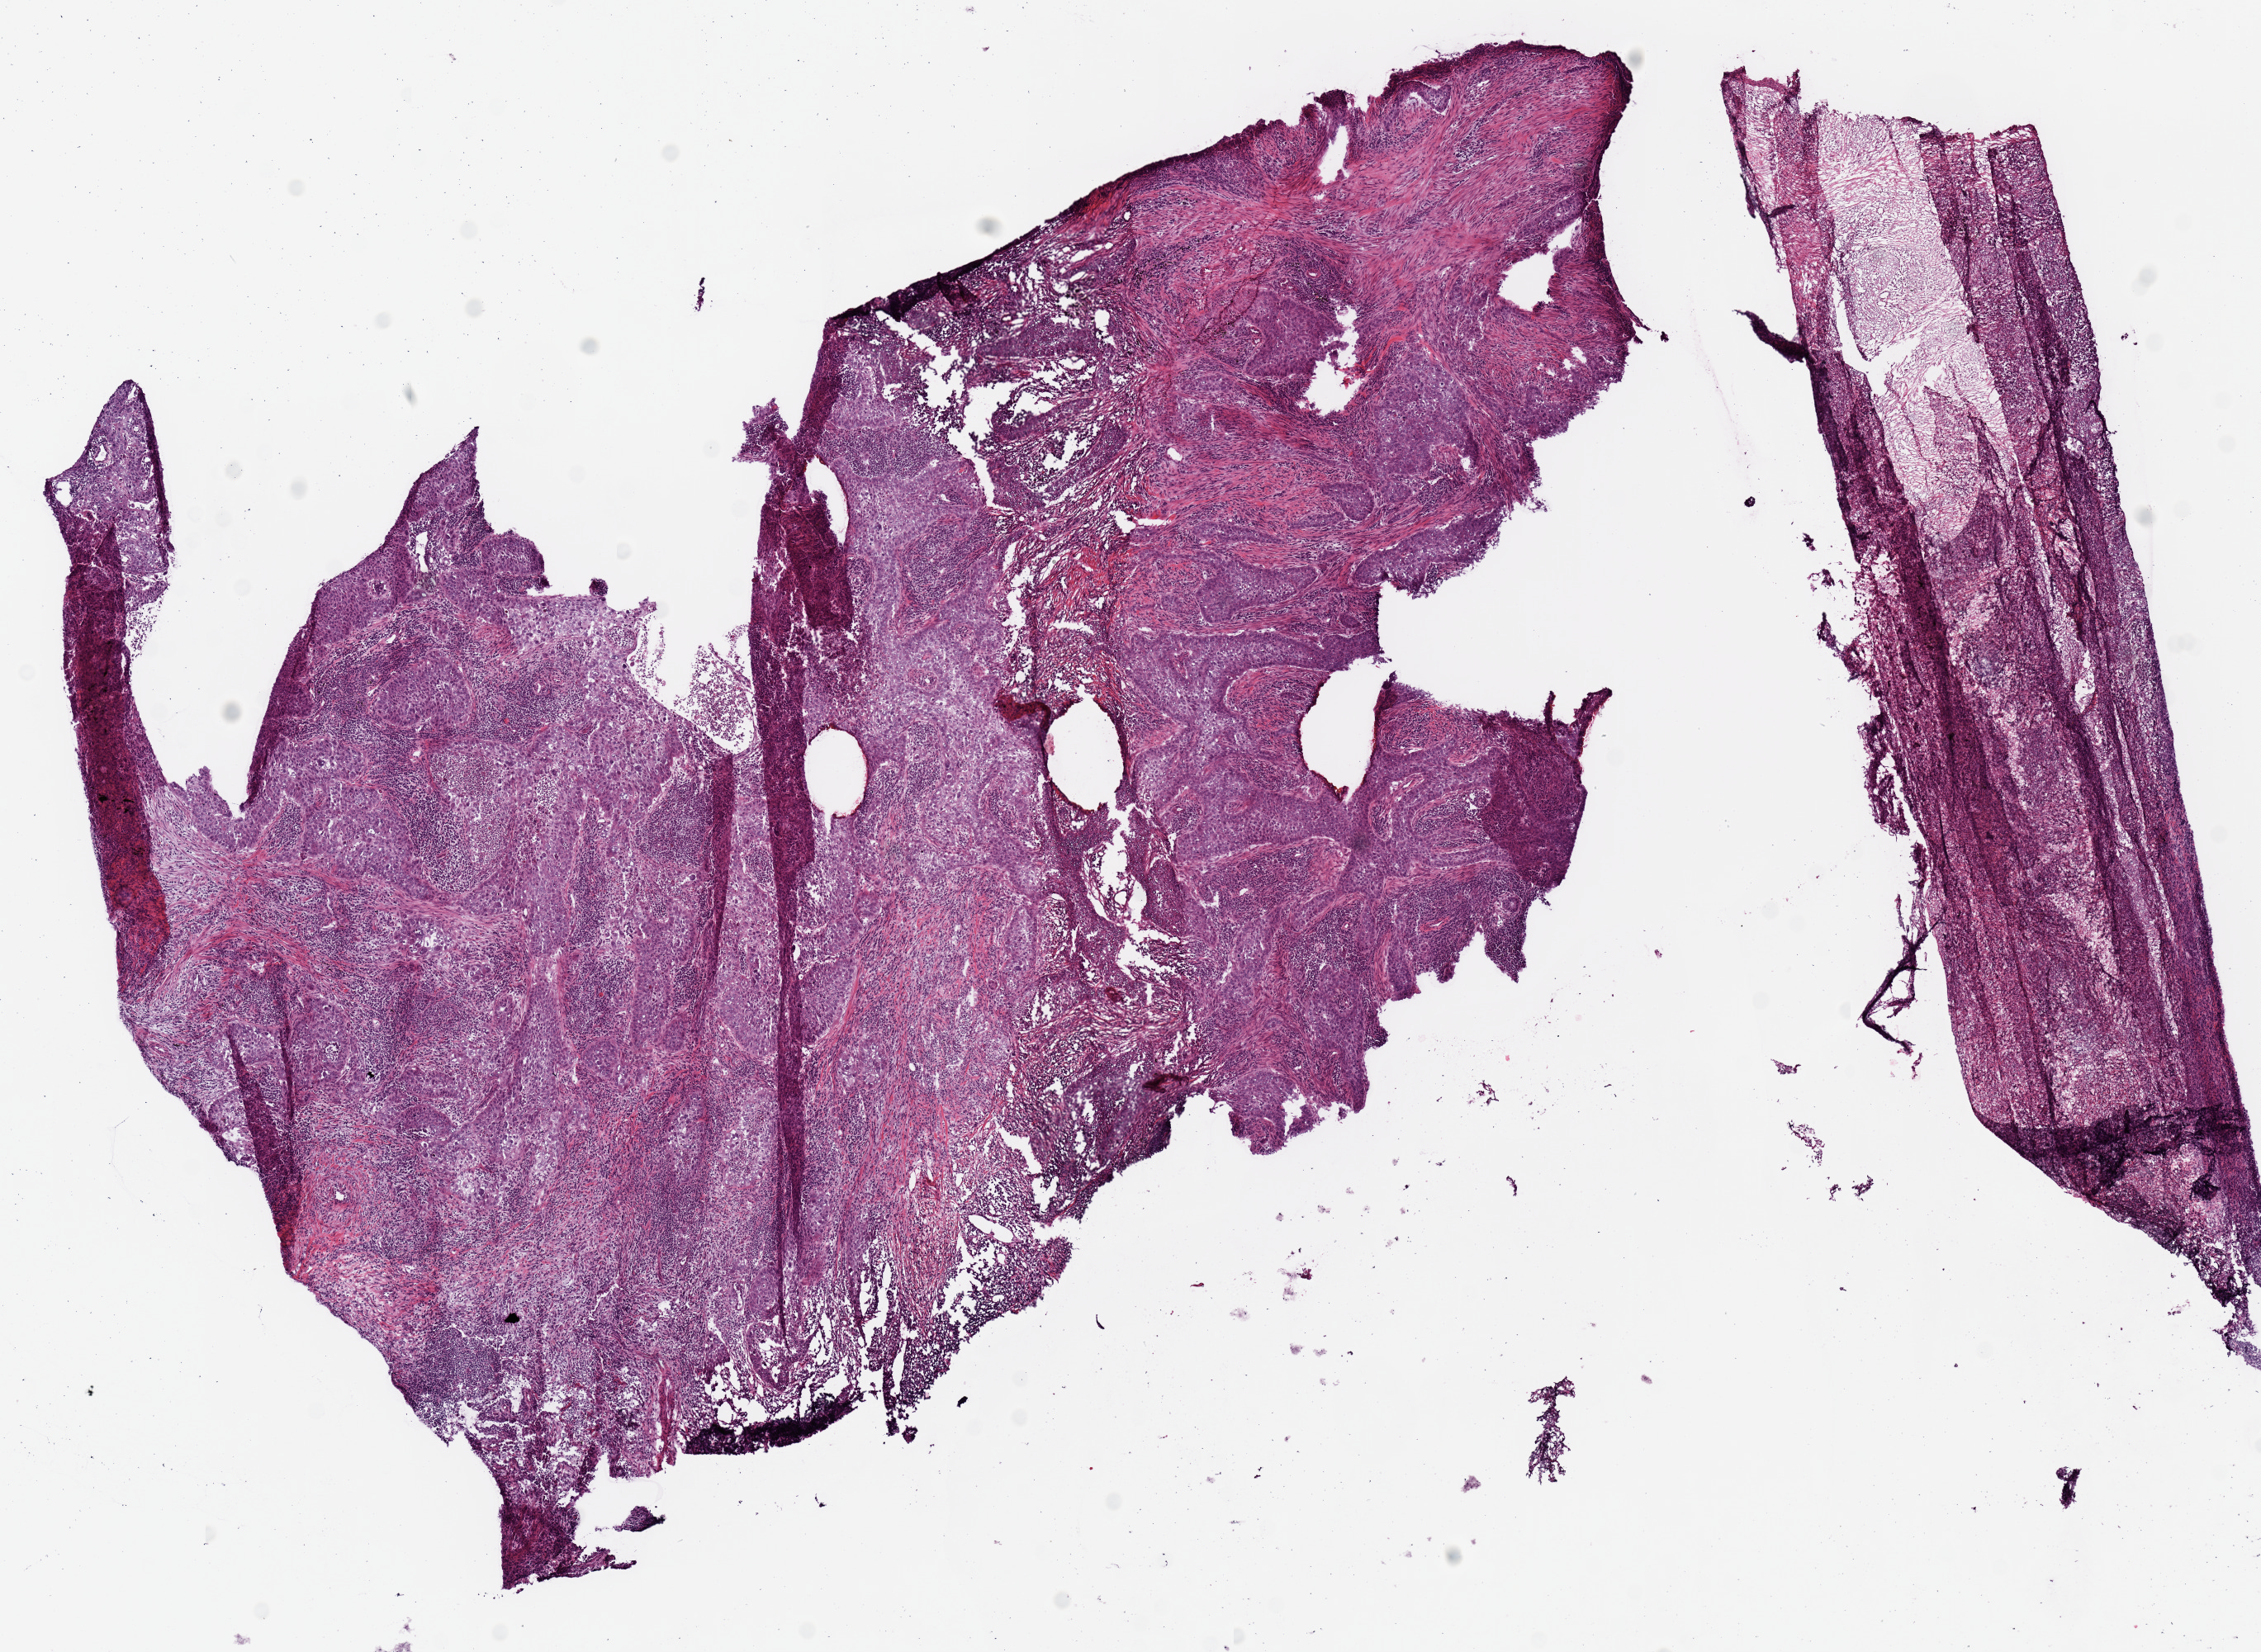
Whole-slide histology image, Hematoxylin and eosin (H&E) stained, whole scanned area (about 10.8 x 7.9 mm, acquisition: 20x scan) shown as a low-resolution overview; frozen section from the top of the tissue portion; primary tumour sample from the lung. Male, age 72 years at initial diagnosis. Slide review estimates, as recorded: tumour cells 75%, tumour nuclei 60%, normal cells 0%, stromal cells 25%, necrosis 0%.
• pathologic diagnosis: Squamous cell carcinoma, NOS (upper lobe, lung)
• AJCC pathologic stage: IIB (6th edition)
• laterality: right